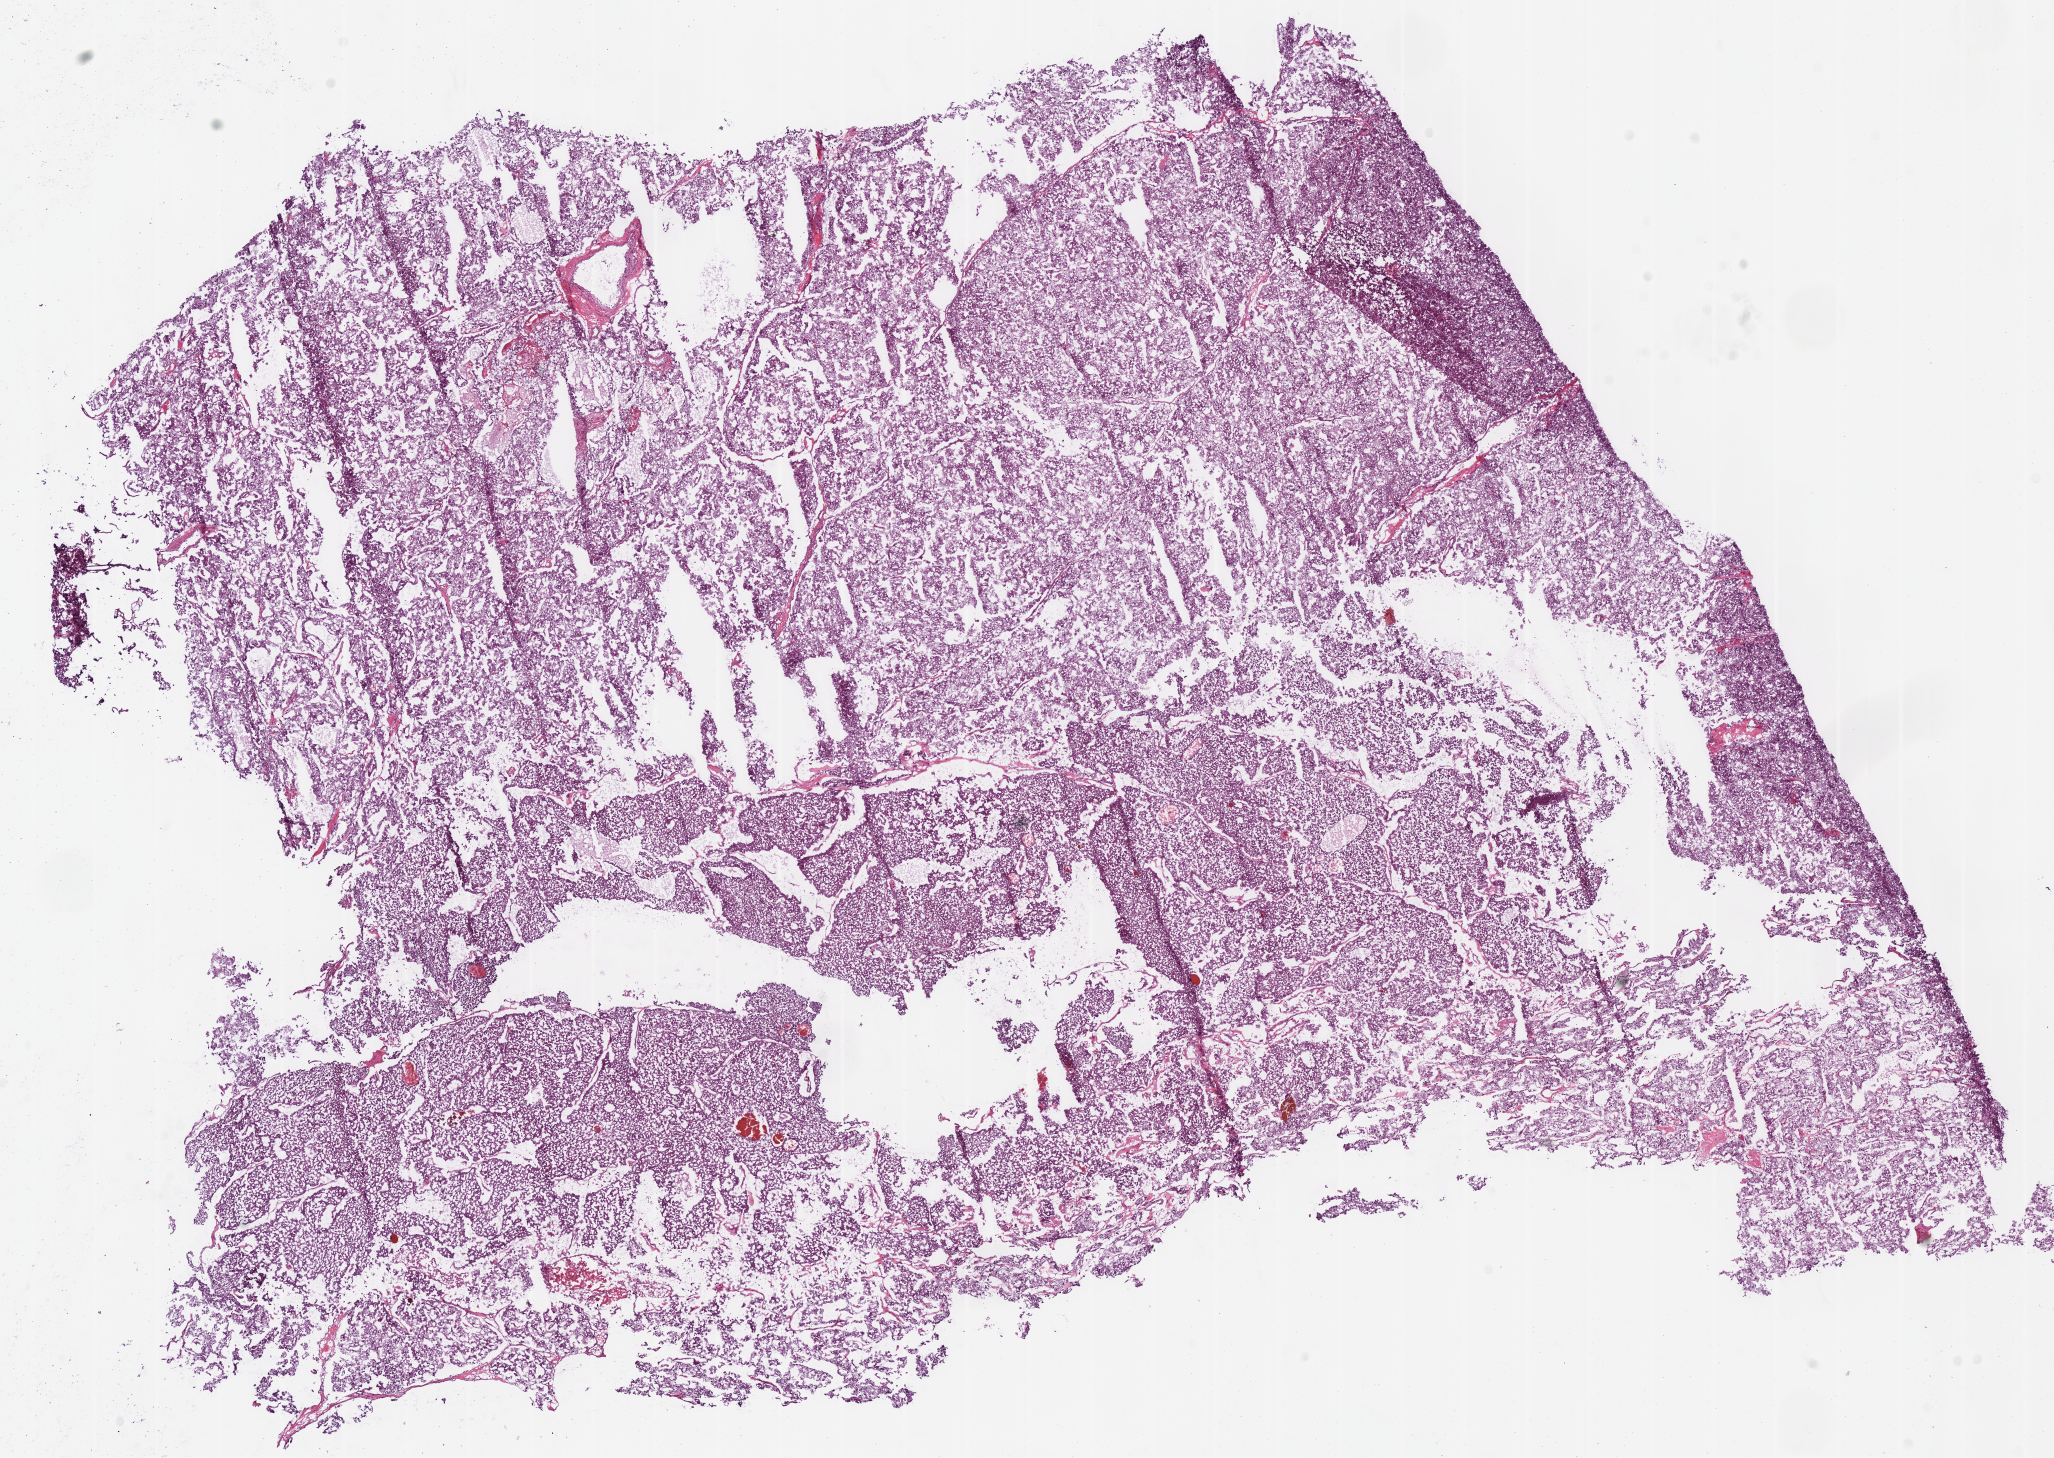
Digitized H&E-stained tissue section (whole slide), whole scanned area (about 16.2 x 11.5 mm, from a 40x scan) shown as a low-resolution overview. Frozen section. Kidney, primary tumour sample. Female patient; age at initial diagnosis 48 years. Slide review estimates, as recorded: tumour cells 100%, tumour nuclei 90%.
Histologic diagnosis: Renal cell carcinoma, chromophobe type.